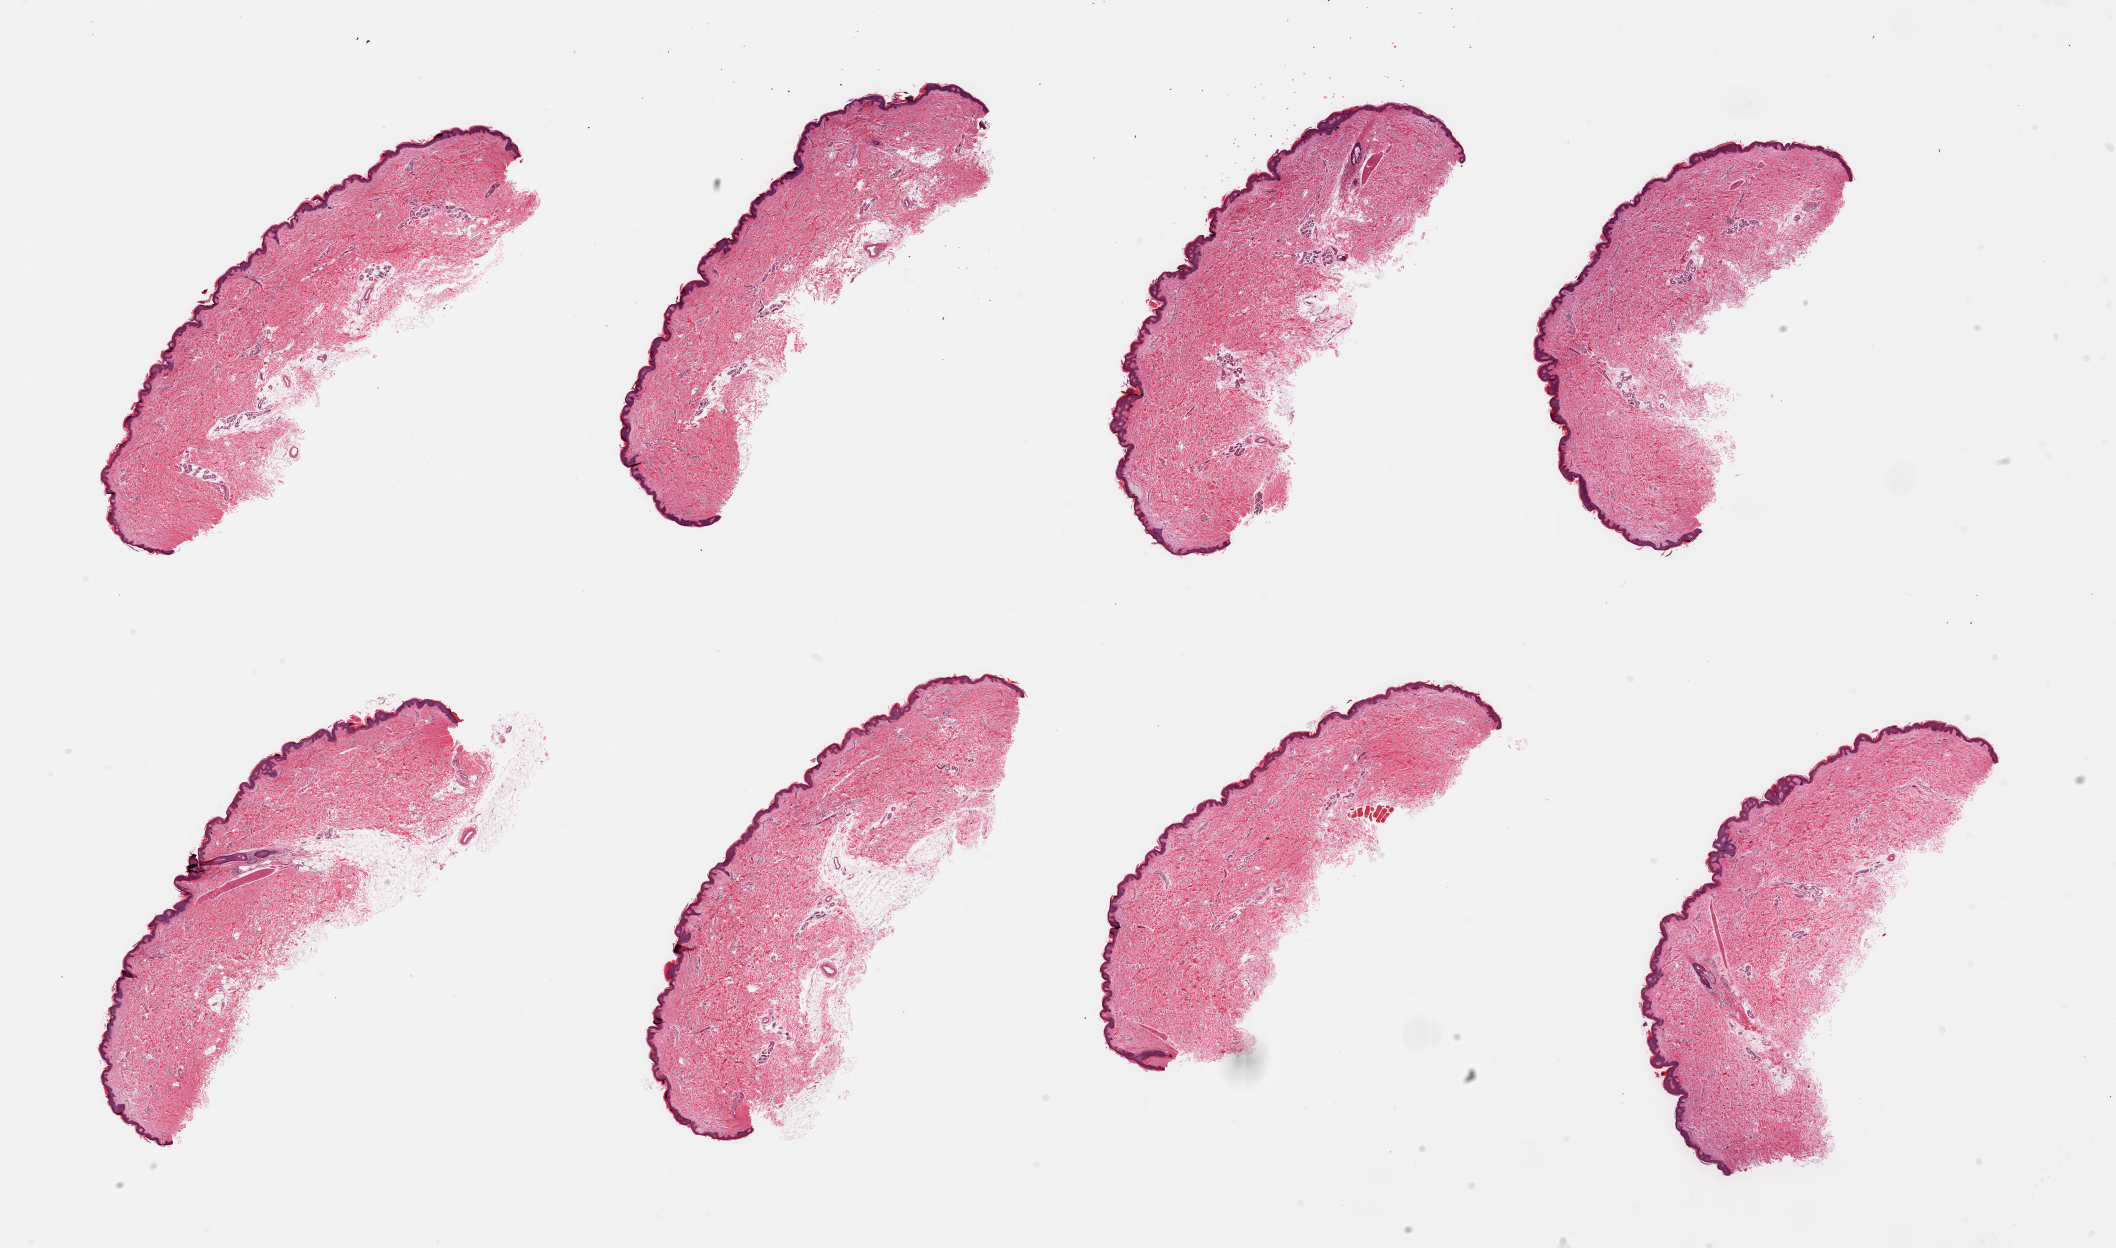
Digitized hematoxylin and eosin (H&E)-stained section — shown as a low-resolution overview of the whole scanned area (about 33.5 x 19.7 mm, slide scanned at 20x); PAXgene-fixed paraffin-embedded (PFPE) section; section of skin of lower leg (target tissue); donor tissue sample. Male donor.
- review note (as recorded): 8 pieces, minimal dermal fat, squamous epithelium is ~50-60 microns